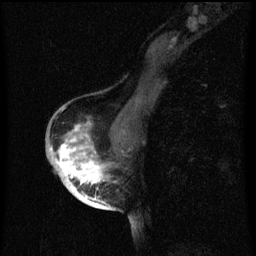
Breast MRI (dynamic contrast-enhanced), one sagittal slice; slice 35 of 60 in the series (ordered by position); dynamic contrast-enhanced series, image 2 of 3 at this slice position (ordered by acquisition); 1.5 T; TE 4.2 ms, TR 8 ms; 256 × 256 image matrix, field of view 180 × 180 mm. Female patient, age 56 years.
Structures marked on this image (semi-automatic segmentation, software-assisted and operator-edited):
- analysis volume of interest (the breast-tissue region the enhancement analysis was run in; not a lesion): bounding box <54,126,120,199> (left, top, right, bottom; pixels)
- tumour enhancement mask (voxels above the 70 % enhancement threshold inside the analysis volume of interest): <55,126,108,199>